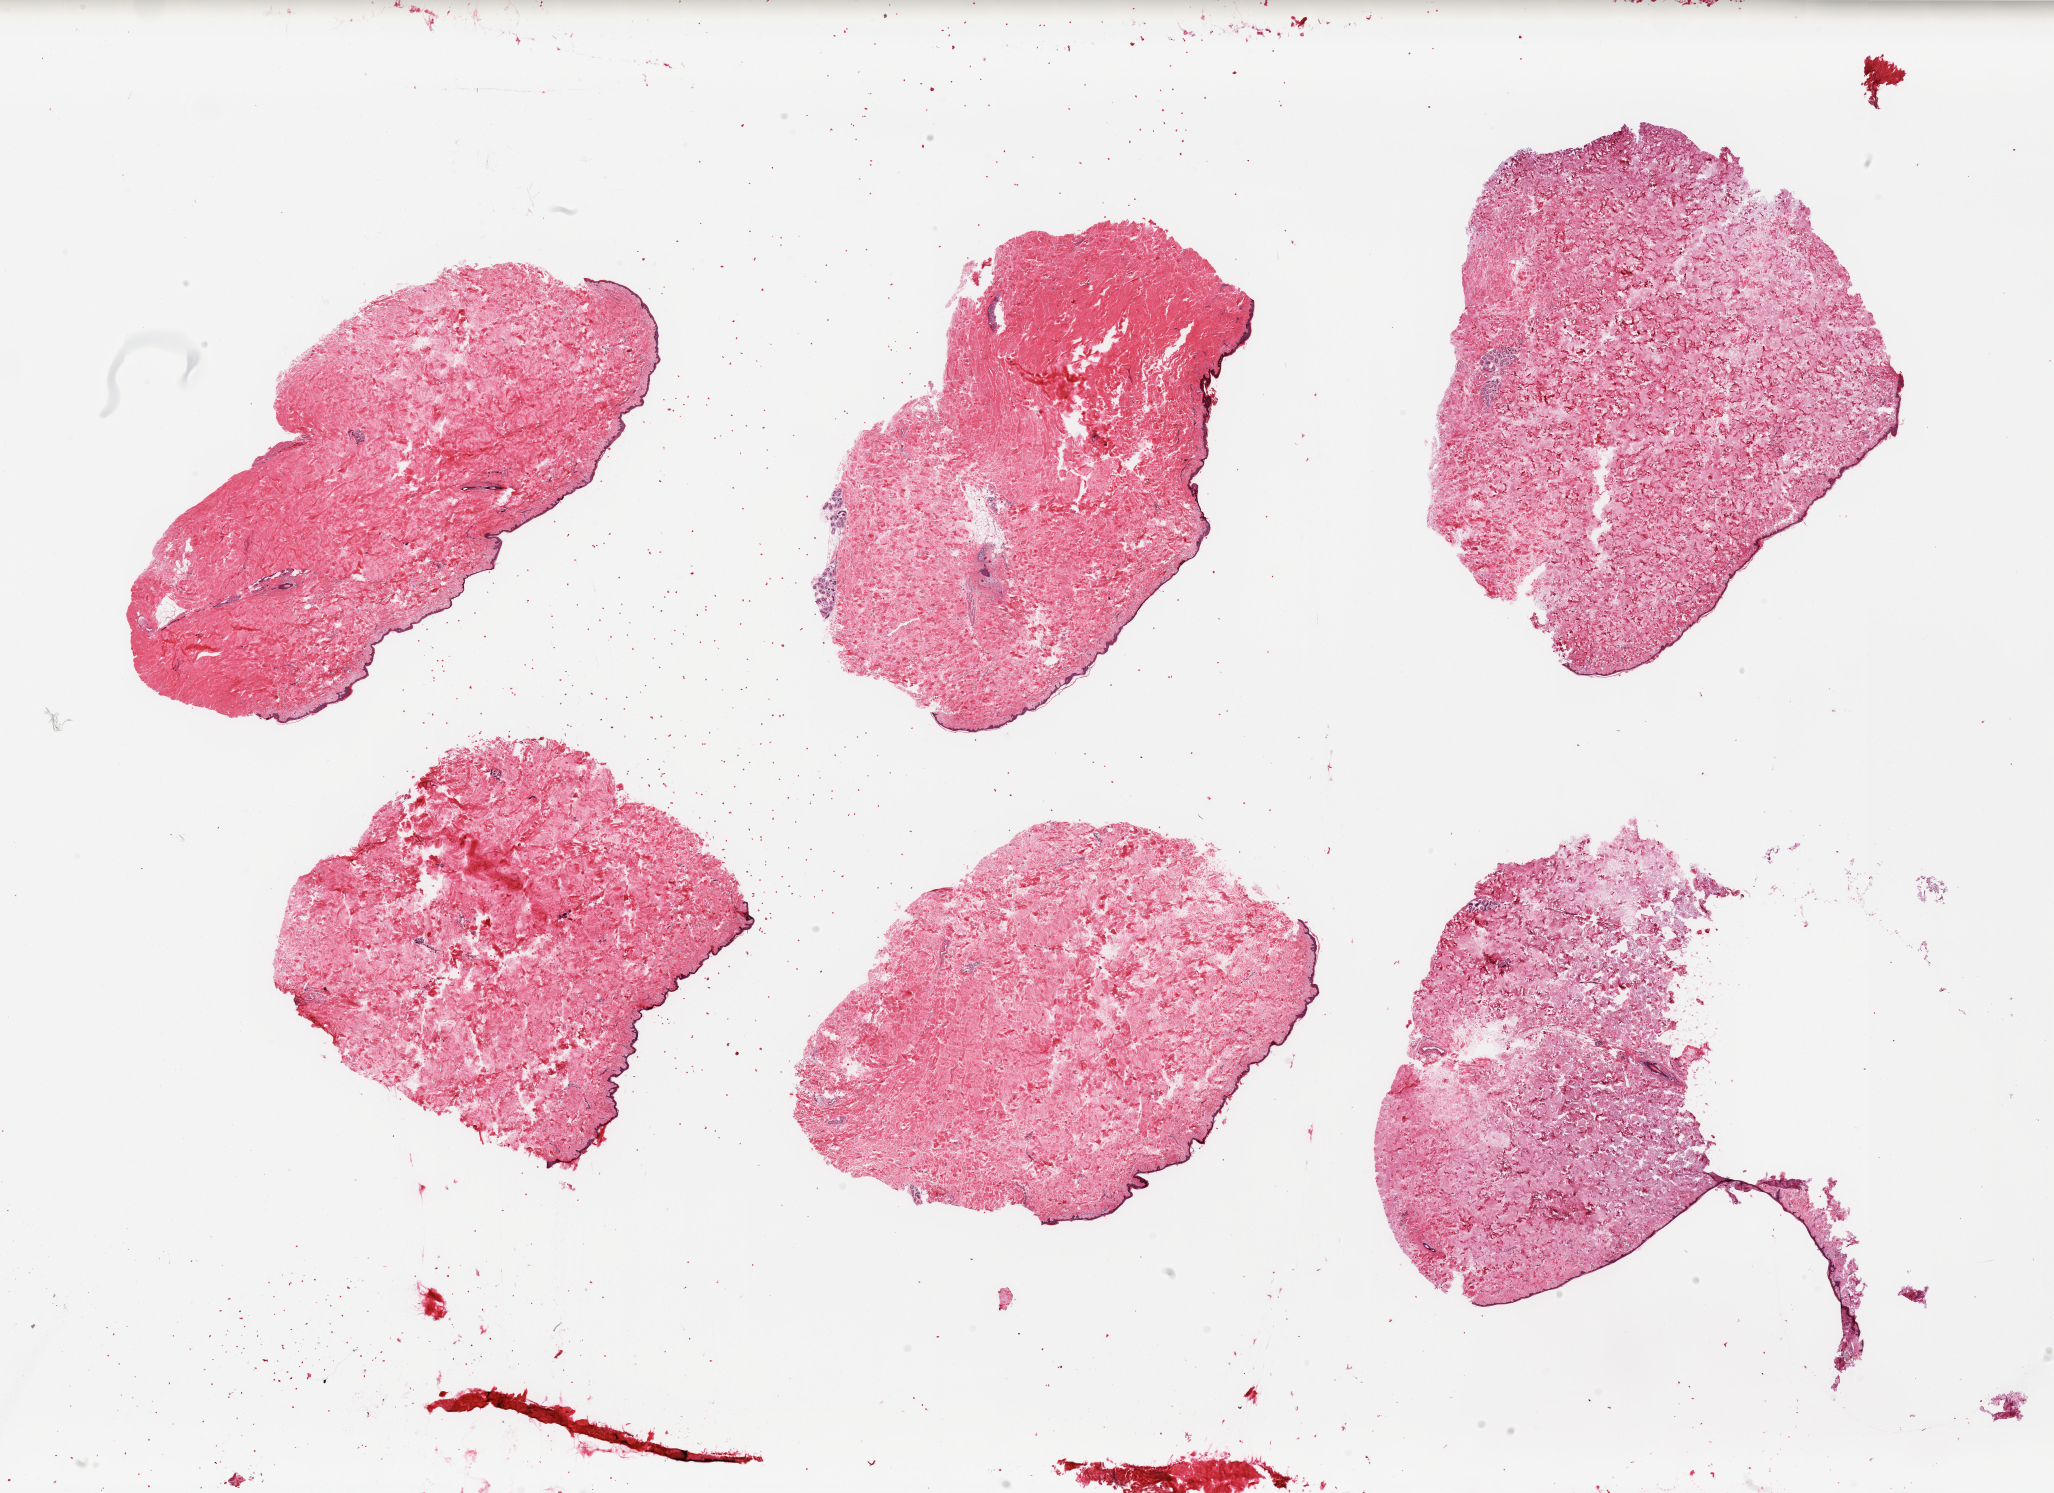
Whole-slide image, hematoxylin and eosin (H&E) stain, brightfield, whole scanned area (about 32.5 x 23.6 mm) shown as a low-resolution overview. PAXgene-fixed, paraffin-embedded tissue. Section of skin of suprapubic region (target tissue). Donor tissue sample.
* review note (as recorded): 6 pieces; well trimmed